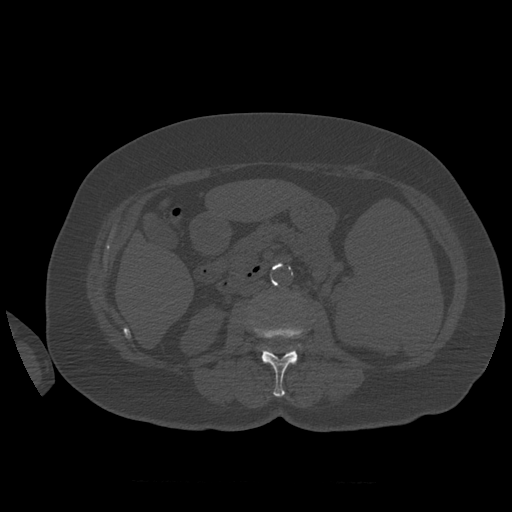
CT including the spine, one axial slice. Position 246 of 399 along the scan axis. Reconstruction kernel STANDARD. 120 kVp. Bone window (W 1800 / L 400 HU). 1.25 mm slice thickness. 512 × 512 image matrix. Patient age 81 years. From the clinical record (not read from this slice): primary cancer: renal; vertebrae with lytic lesions (as recorded): L1.
Structures marked on this image (semi-automatic segmentation, software-assisted and operator-edited):
- L2 vertebra: bounding box [x1, y1, x2, y2] px = [251, 322, 309, 397]